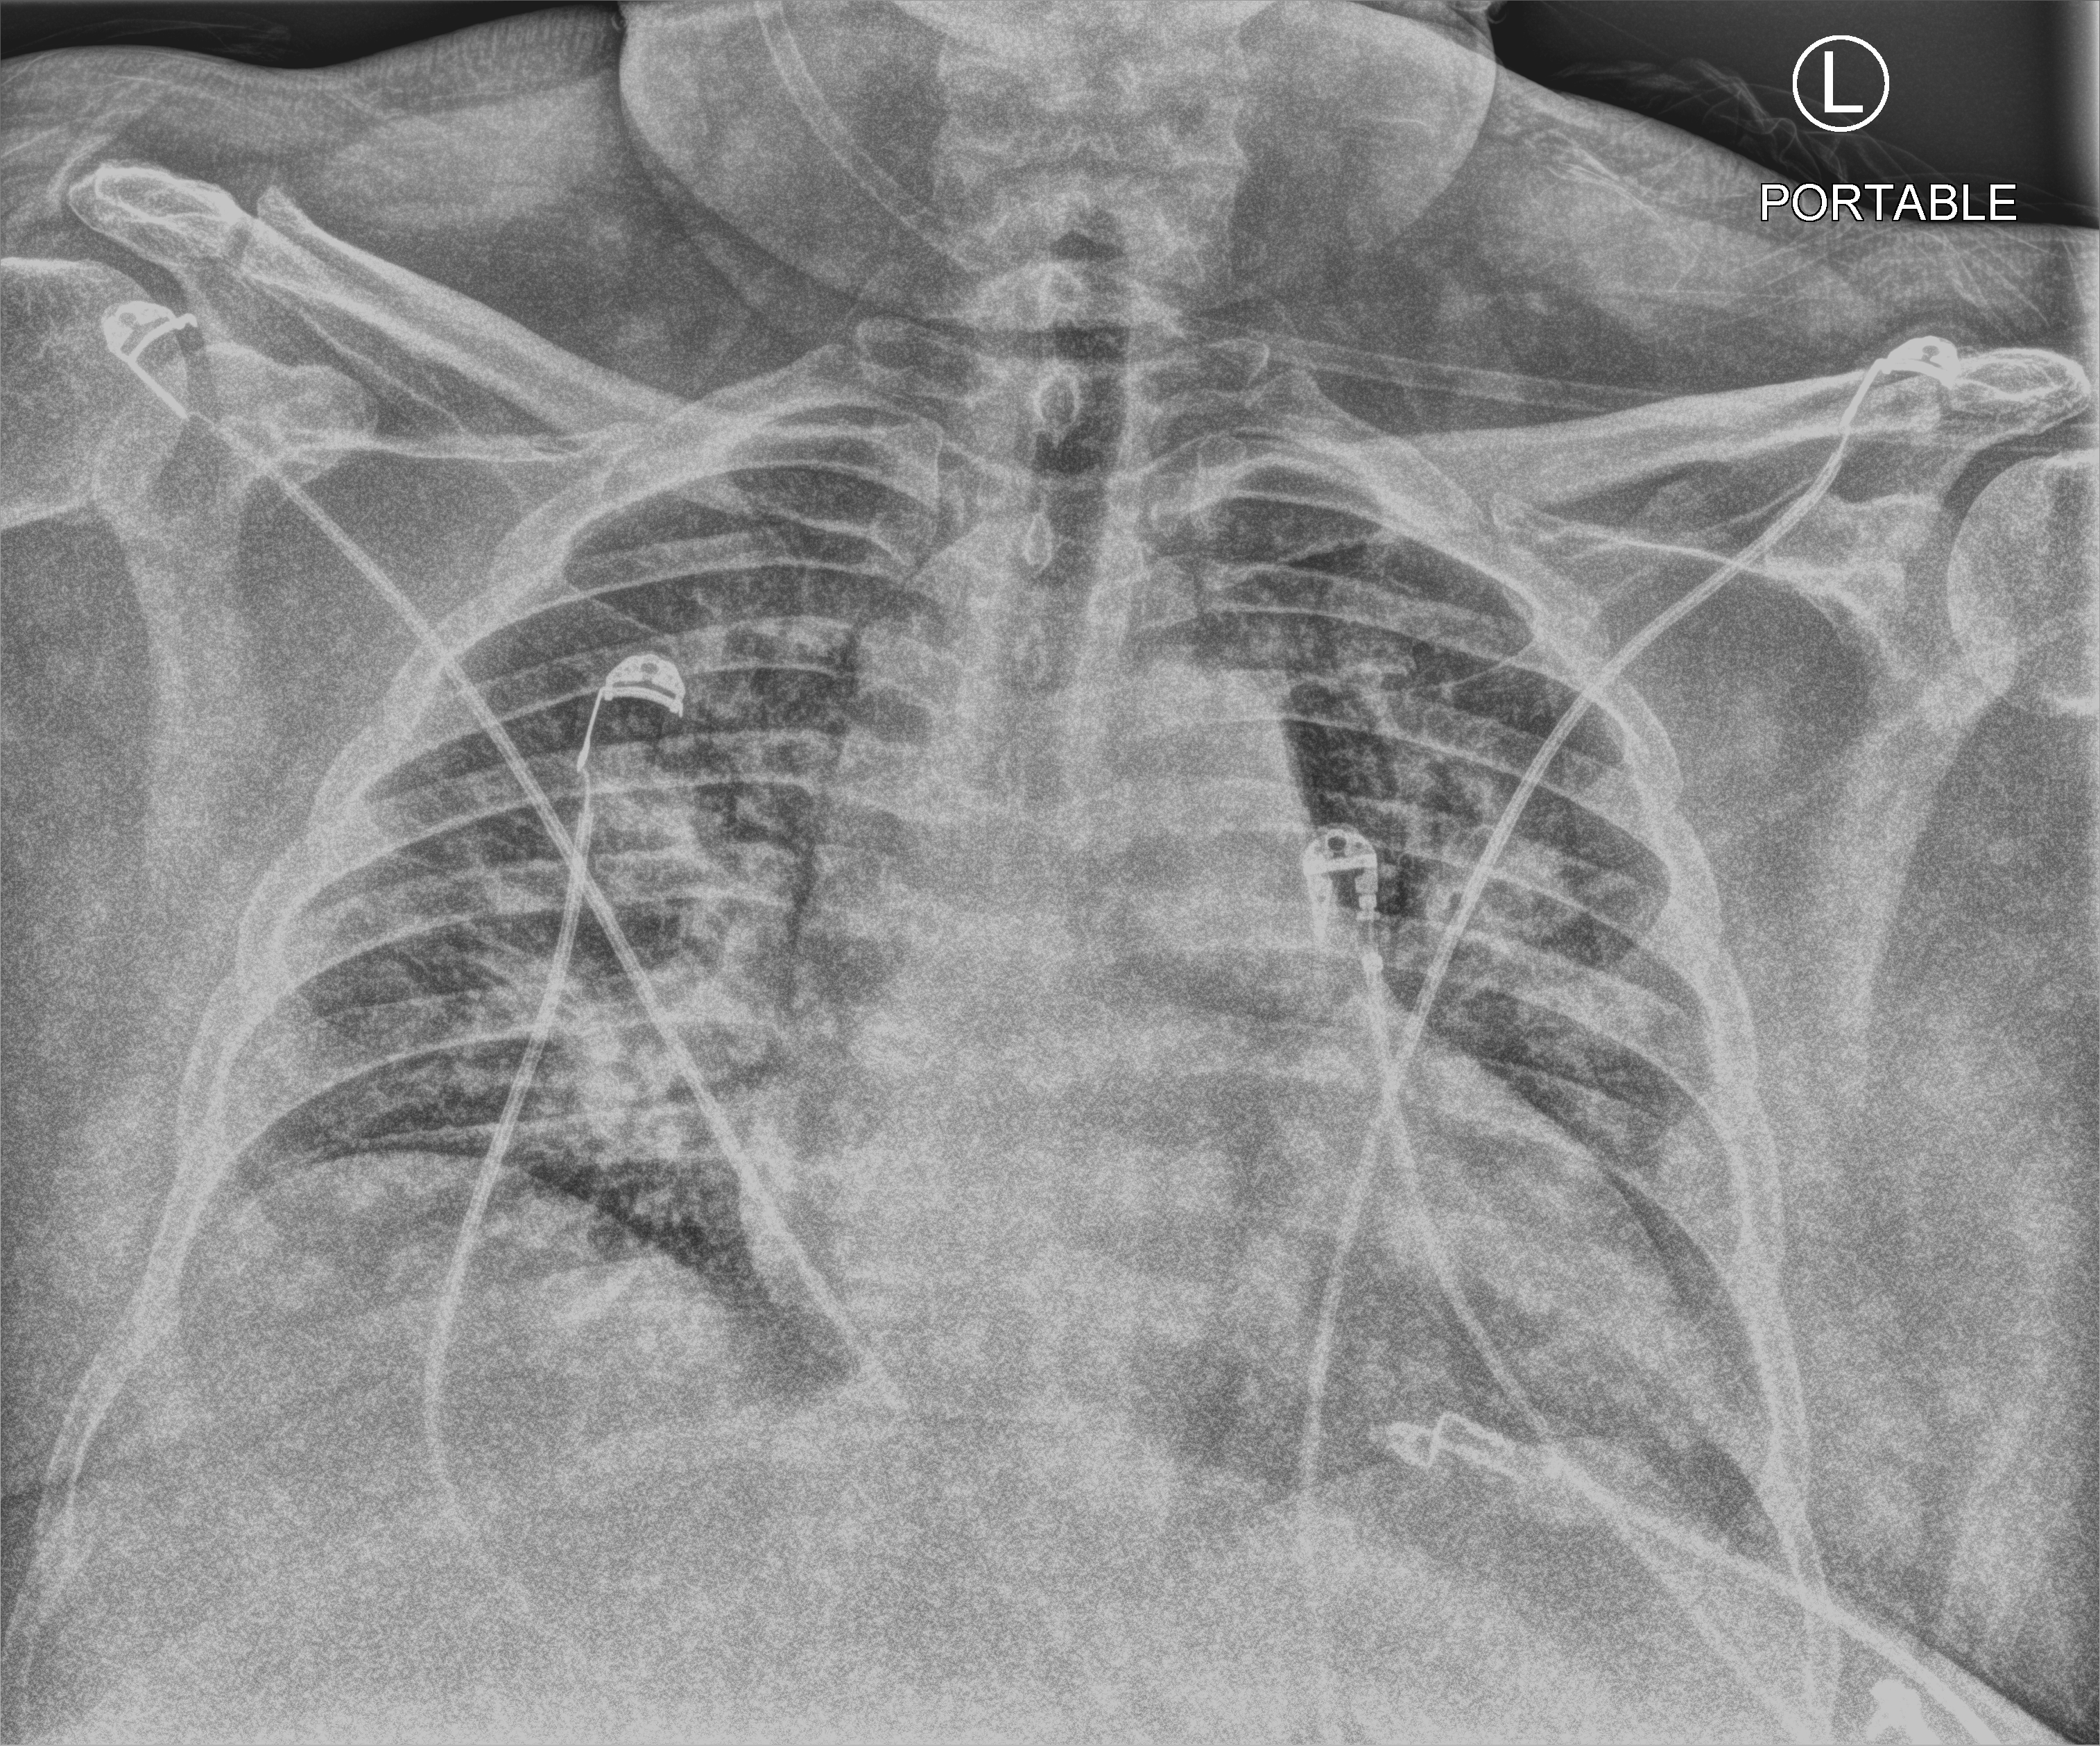
Chest X-ray (portable); anteroposterior (AP) projection. Male patient hospitalised with COVID-19, age 18–59 years.
Hospital-stay facts (about this admission, not read from this image; timing relative to this image not recorded): length of hospital stay: 28 days; admitted to intensive care during this hospital stay: yes.